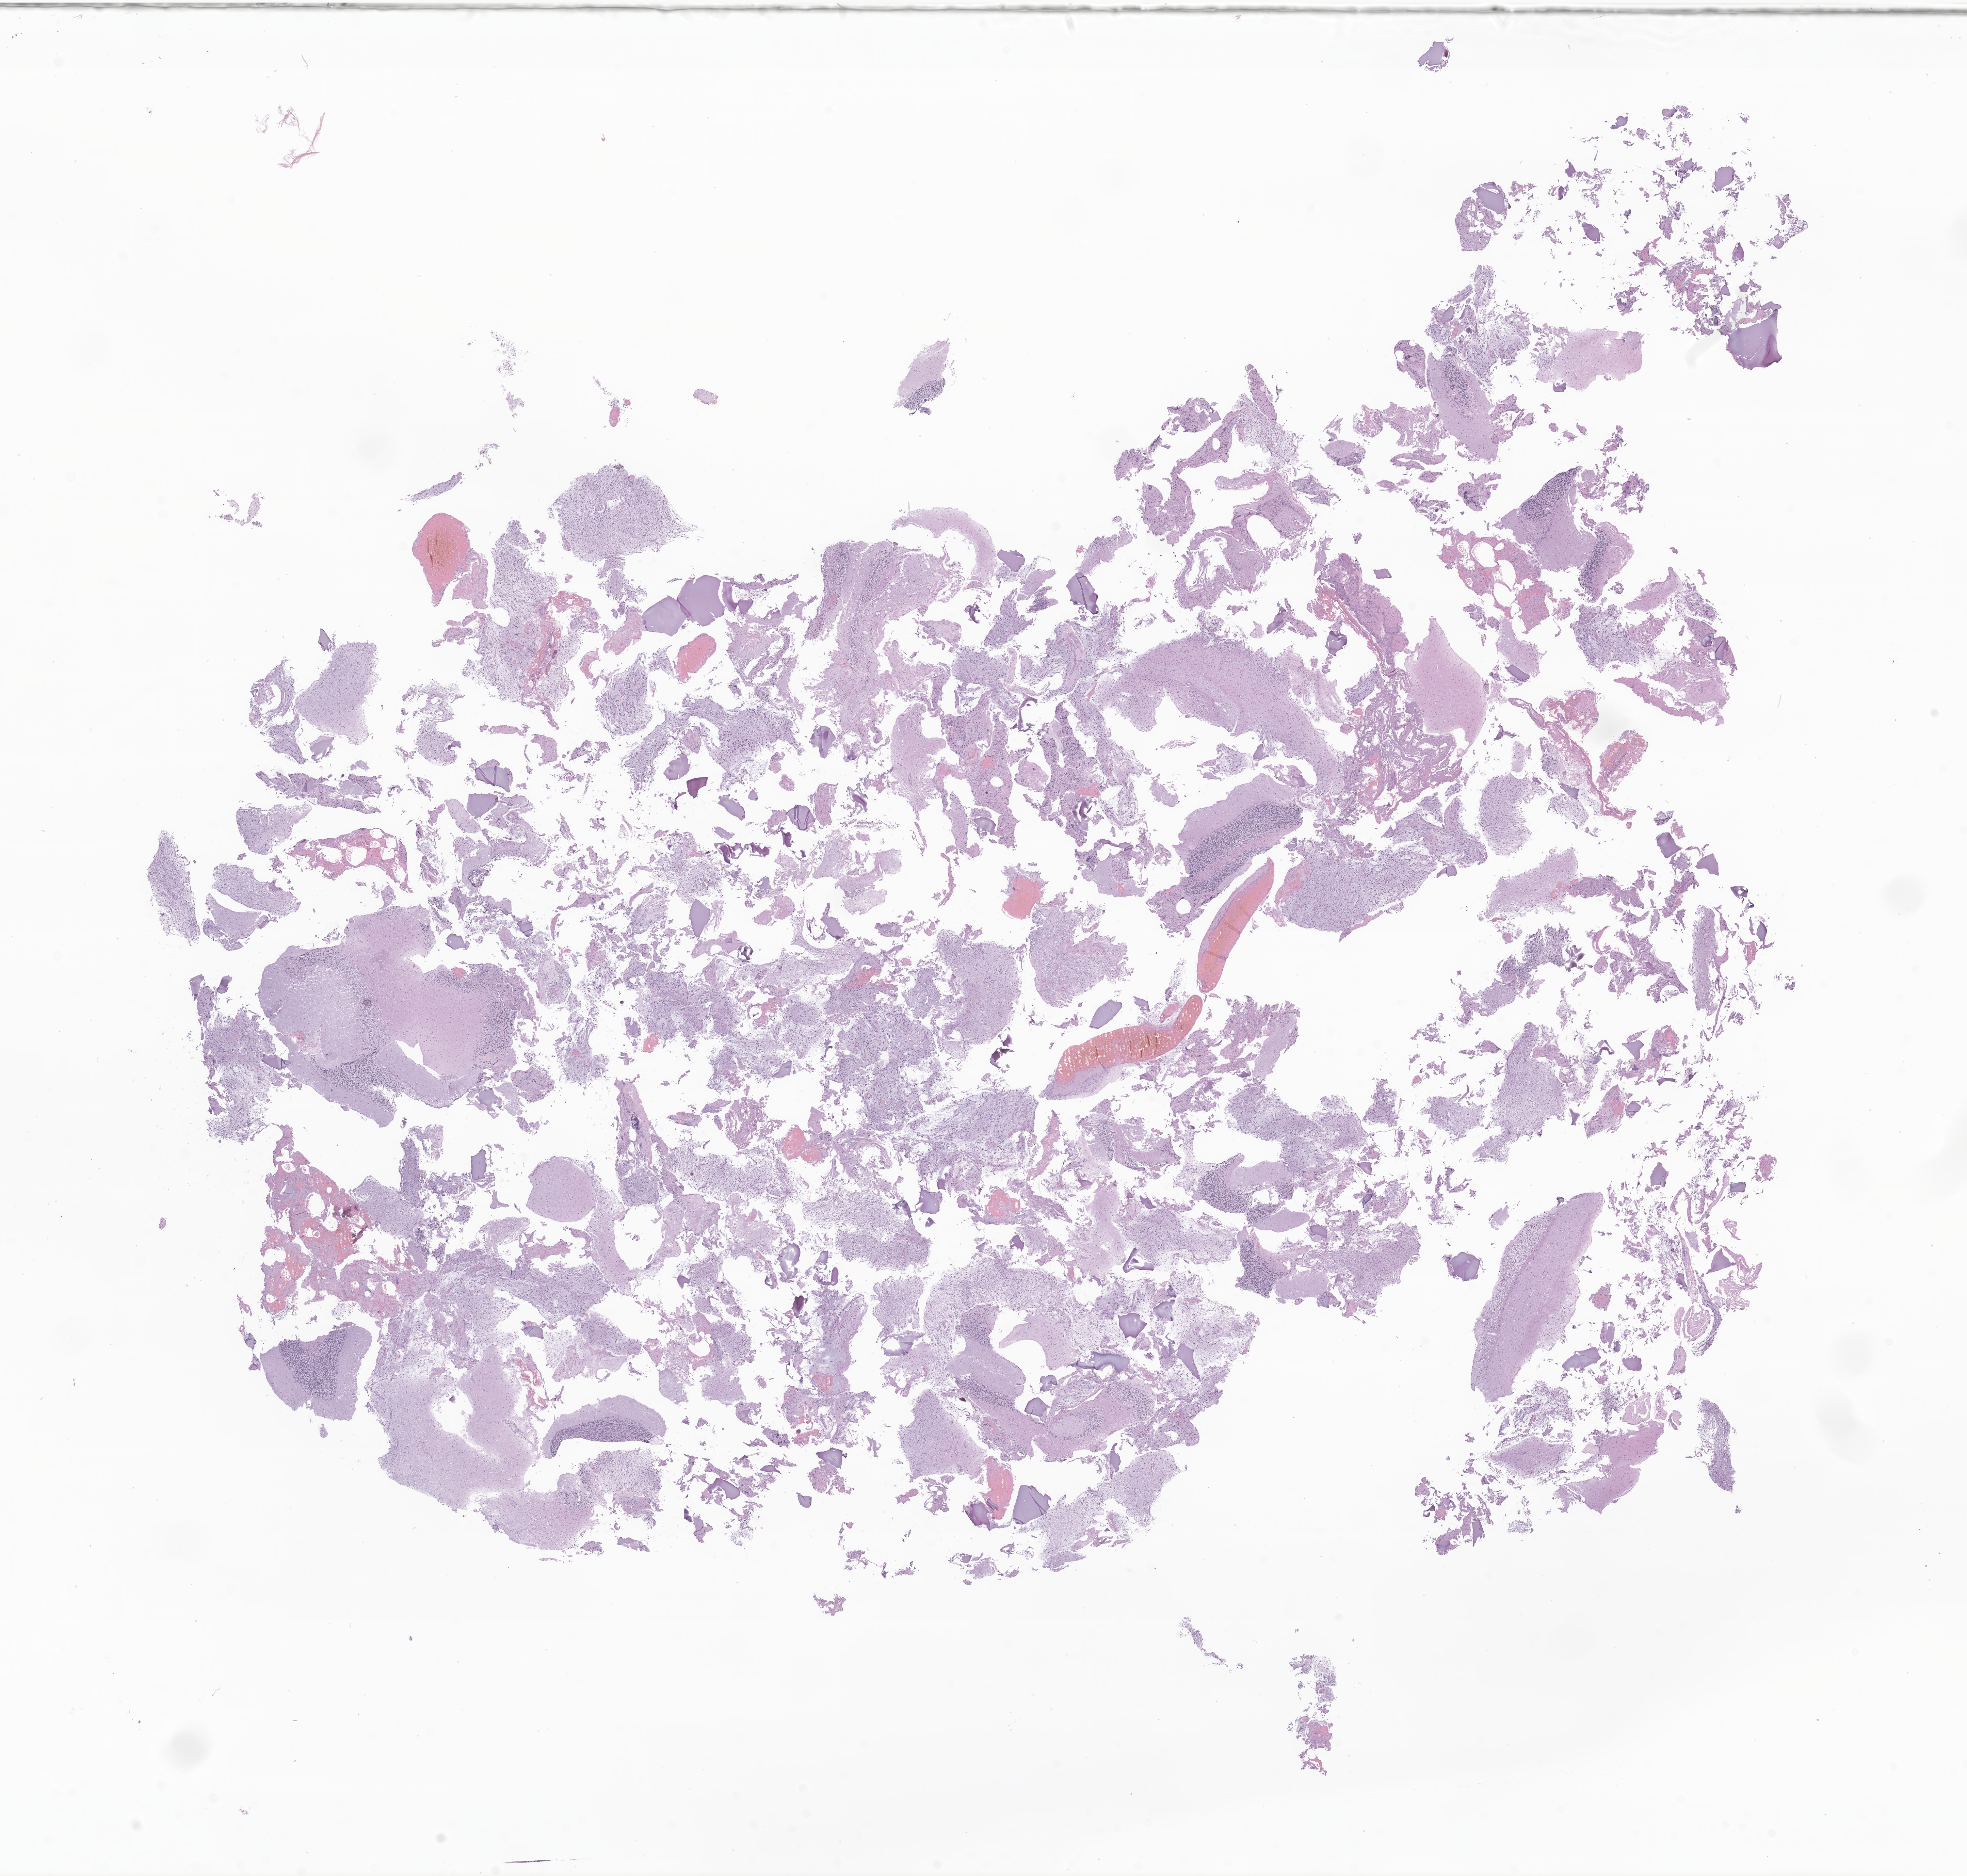
Hematoxylin and eosin (H&E) whole-slide image of tumor tissue from the brain, whole scanned area (about 24.4 x 23.2 mm) shown as a low-resolution overview; FFPE section. Patient: male, age 102 months (8 years 6 months).
Recorded diagnosis: Astrocytoma, NOS.